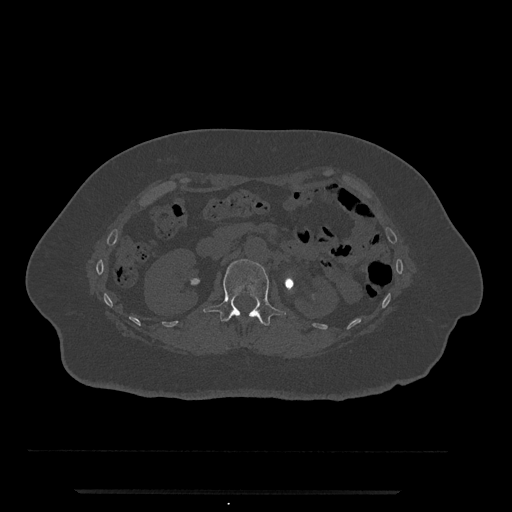
CT including the spine, one axial slice; bone window (W 1800 / L 400 HU); 0.5 mm slice thickness; 512 × 512 image matrix. Patient: female, 51 years. Case-level facts recorded for this patient, not image findings: primary cancer: neuro.
Annotated regions visible in this slice (semi-automatic segmentation, software-assisted and operator-edited):
- L1 vertebra: bounding box <203,259,286,326> (left, top, right, bottom; pixels)